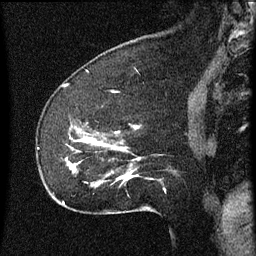
Breast MRI (dynamic contrast-enhanced), one sagittal slice. Position 18 of 60 along the scan axis. Dynamic contrast-enhanced series, image 2 of 3 at this slice position (ordered by acquisition). 1.5 T. TE 4.2 ms, TR 8 ms. 2 mm slice thickness. 256 × 256 image matrix, field of view 180 × 180 mm. Female patient, age 52 years.
Annotated regions visible in this slice (semi-automatically segmented with operator editing):
- analysis volume of interest (the breast-tissue region the enhancement analysis was run in; not a lesion): bounding box (x1, y1, x2, y2) in pixels: (54, 118, 166, 207)
- tumour enhancement mask (voxels above the 70 % enhancement threshold inside the analysis volume of interest): (67, 126, 138, 179)